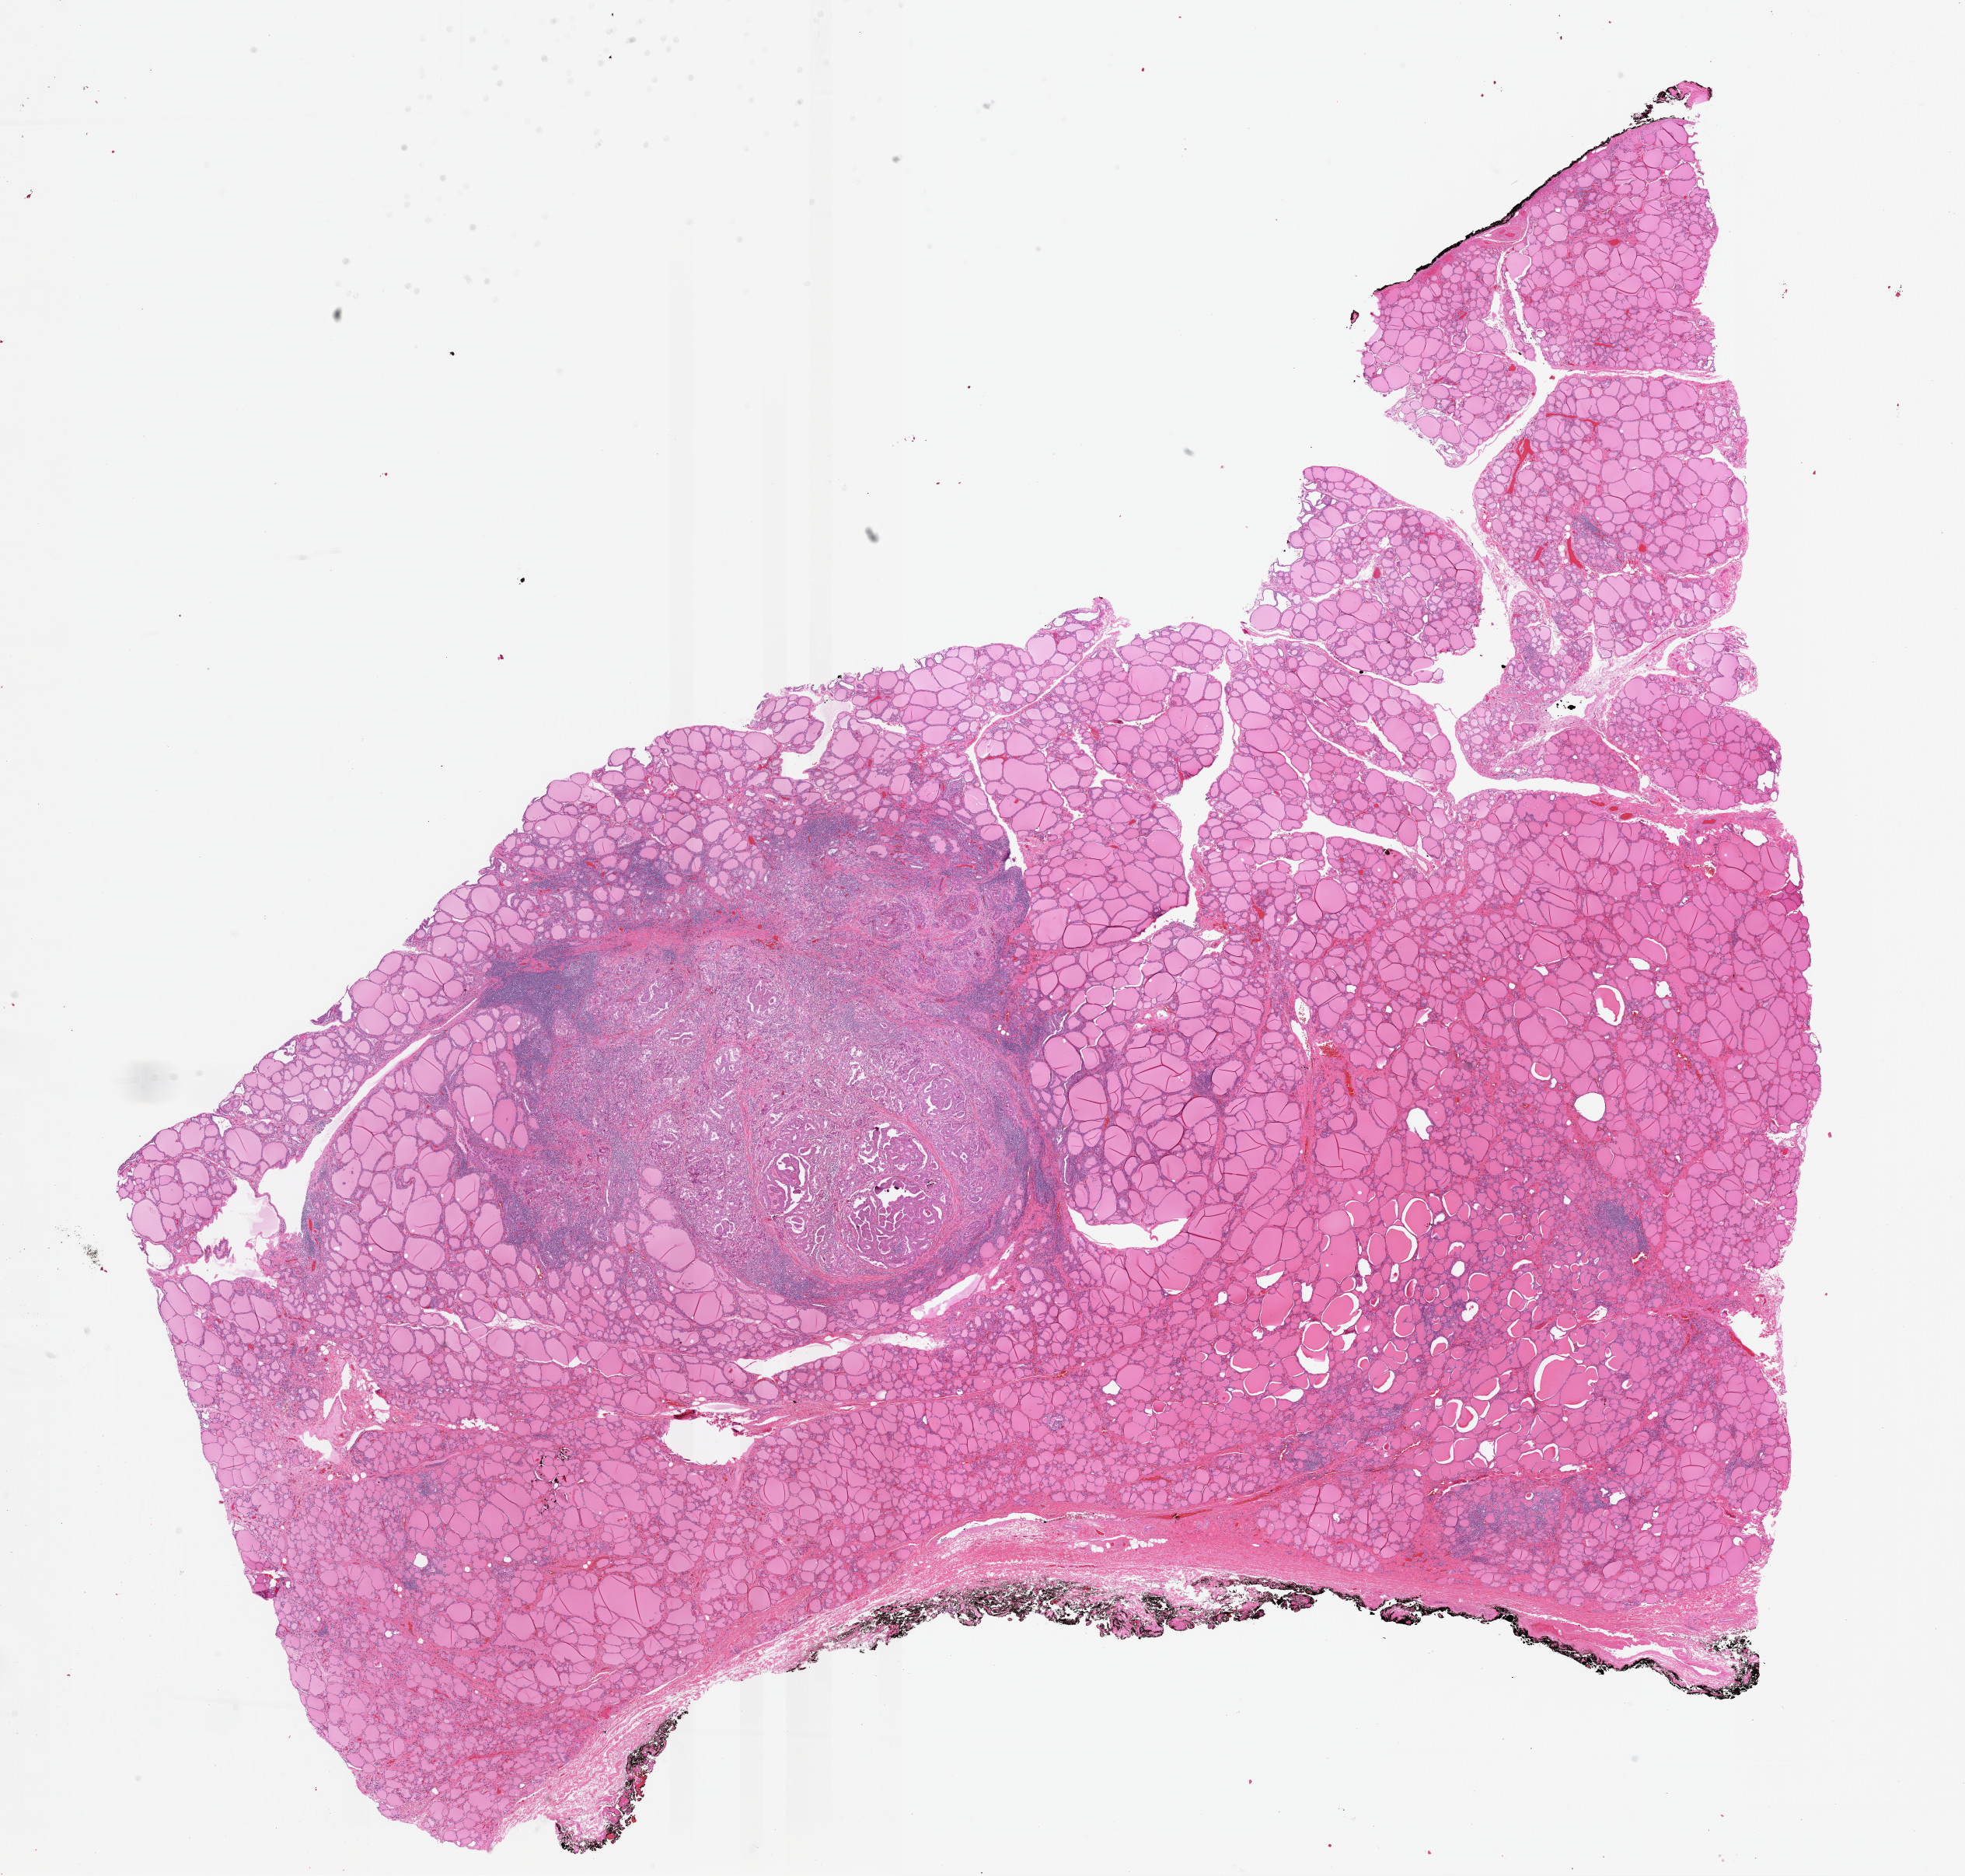
Digitized H&E-stained tissue section (whole slide) — a low-resolution overview of the entire scanned area, about 20.0 x 19.1 mm. Formalin-fixed paraffin-embedded (FFPE) diagnostic section. Thyroid, primary tumour sample. Patient: male, age at initial diagnosis 39 years.
* laterality: midline
* pathologic diagnosis: Papillary carcinoma, columnar cell
* AJCC pathologic stage: I